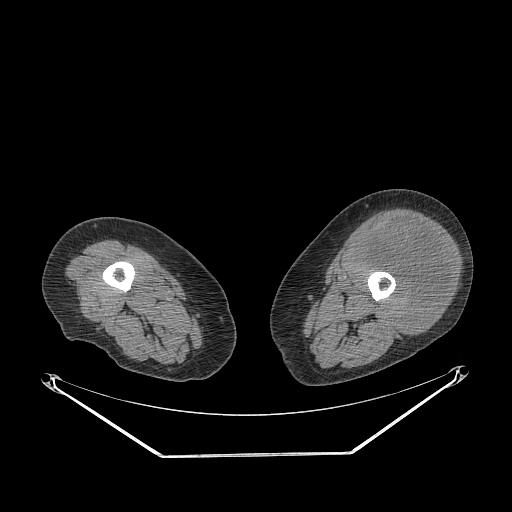
CT of an extremity soft-tissue mass (from a PET/CT study), one axial slice; slice 218 of 267 in the series (ordered by position); 140 kVp; soft-tissue window (W 400 / L 40 HU); 3.75 mm slice thickness; 512 × 512 image matrix. Female patient. Case-level facts recorded for this patient, not image findings: histological type: undifferentiated – high grade; grade: high; site of the primary tumour: left thigh.
Annotated regions visible in this slice (expert contour drawn on MRI and transferred to this co-registered scan by the dataset authors):
- gross tumour volume including surrounding oedema: bounding box <358,217,453,334> (left, top, right, bottom; pixels)
- gross tumour volume (mass): <358,217,453,334>